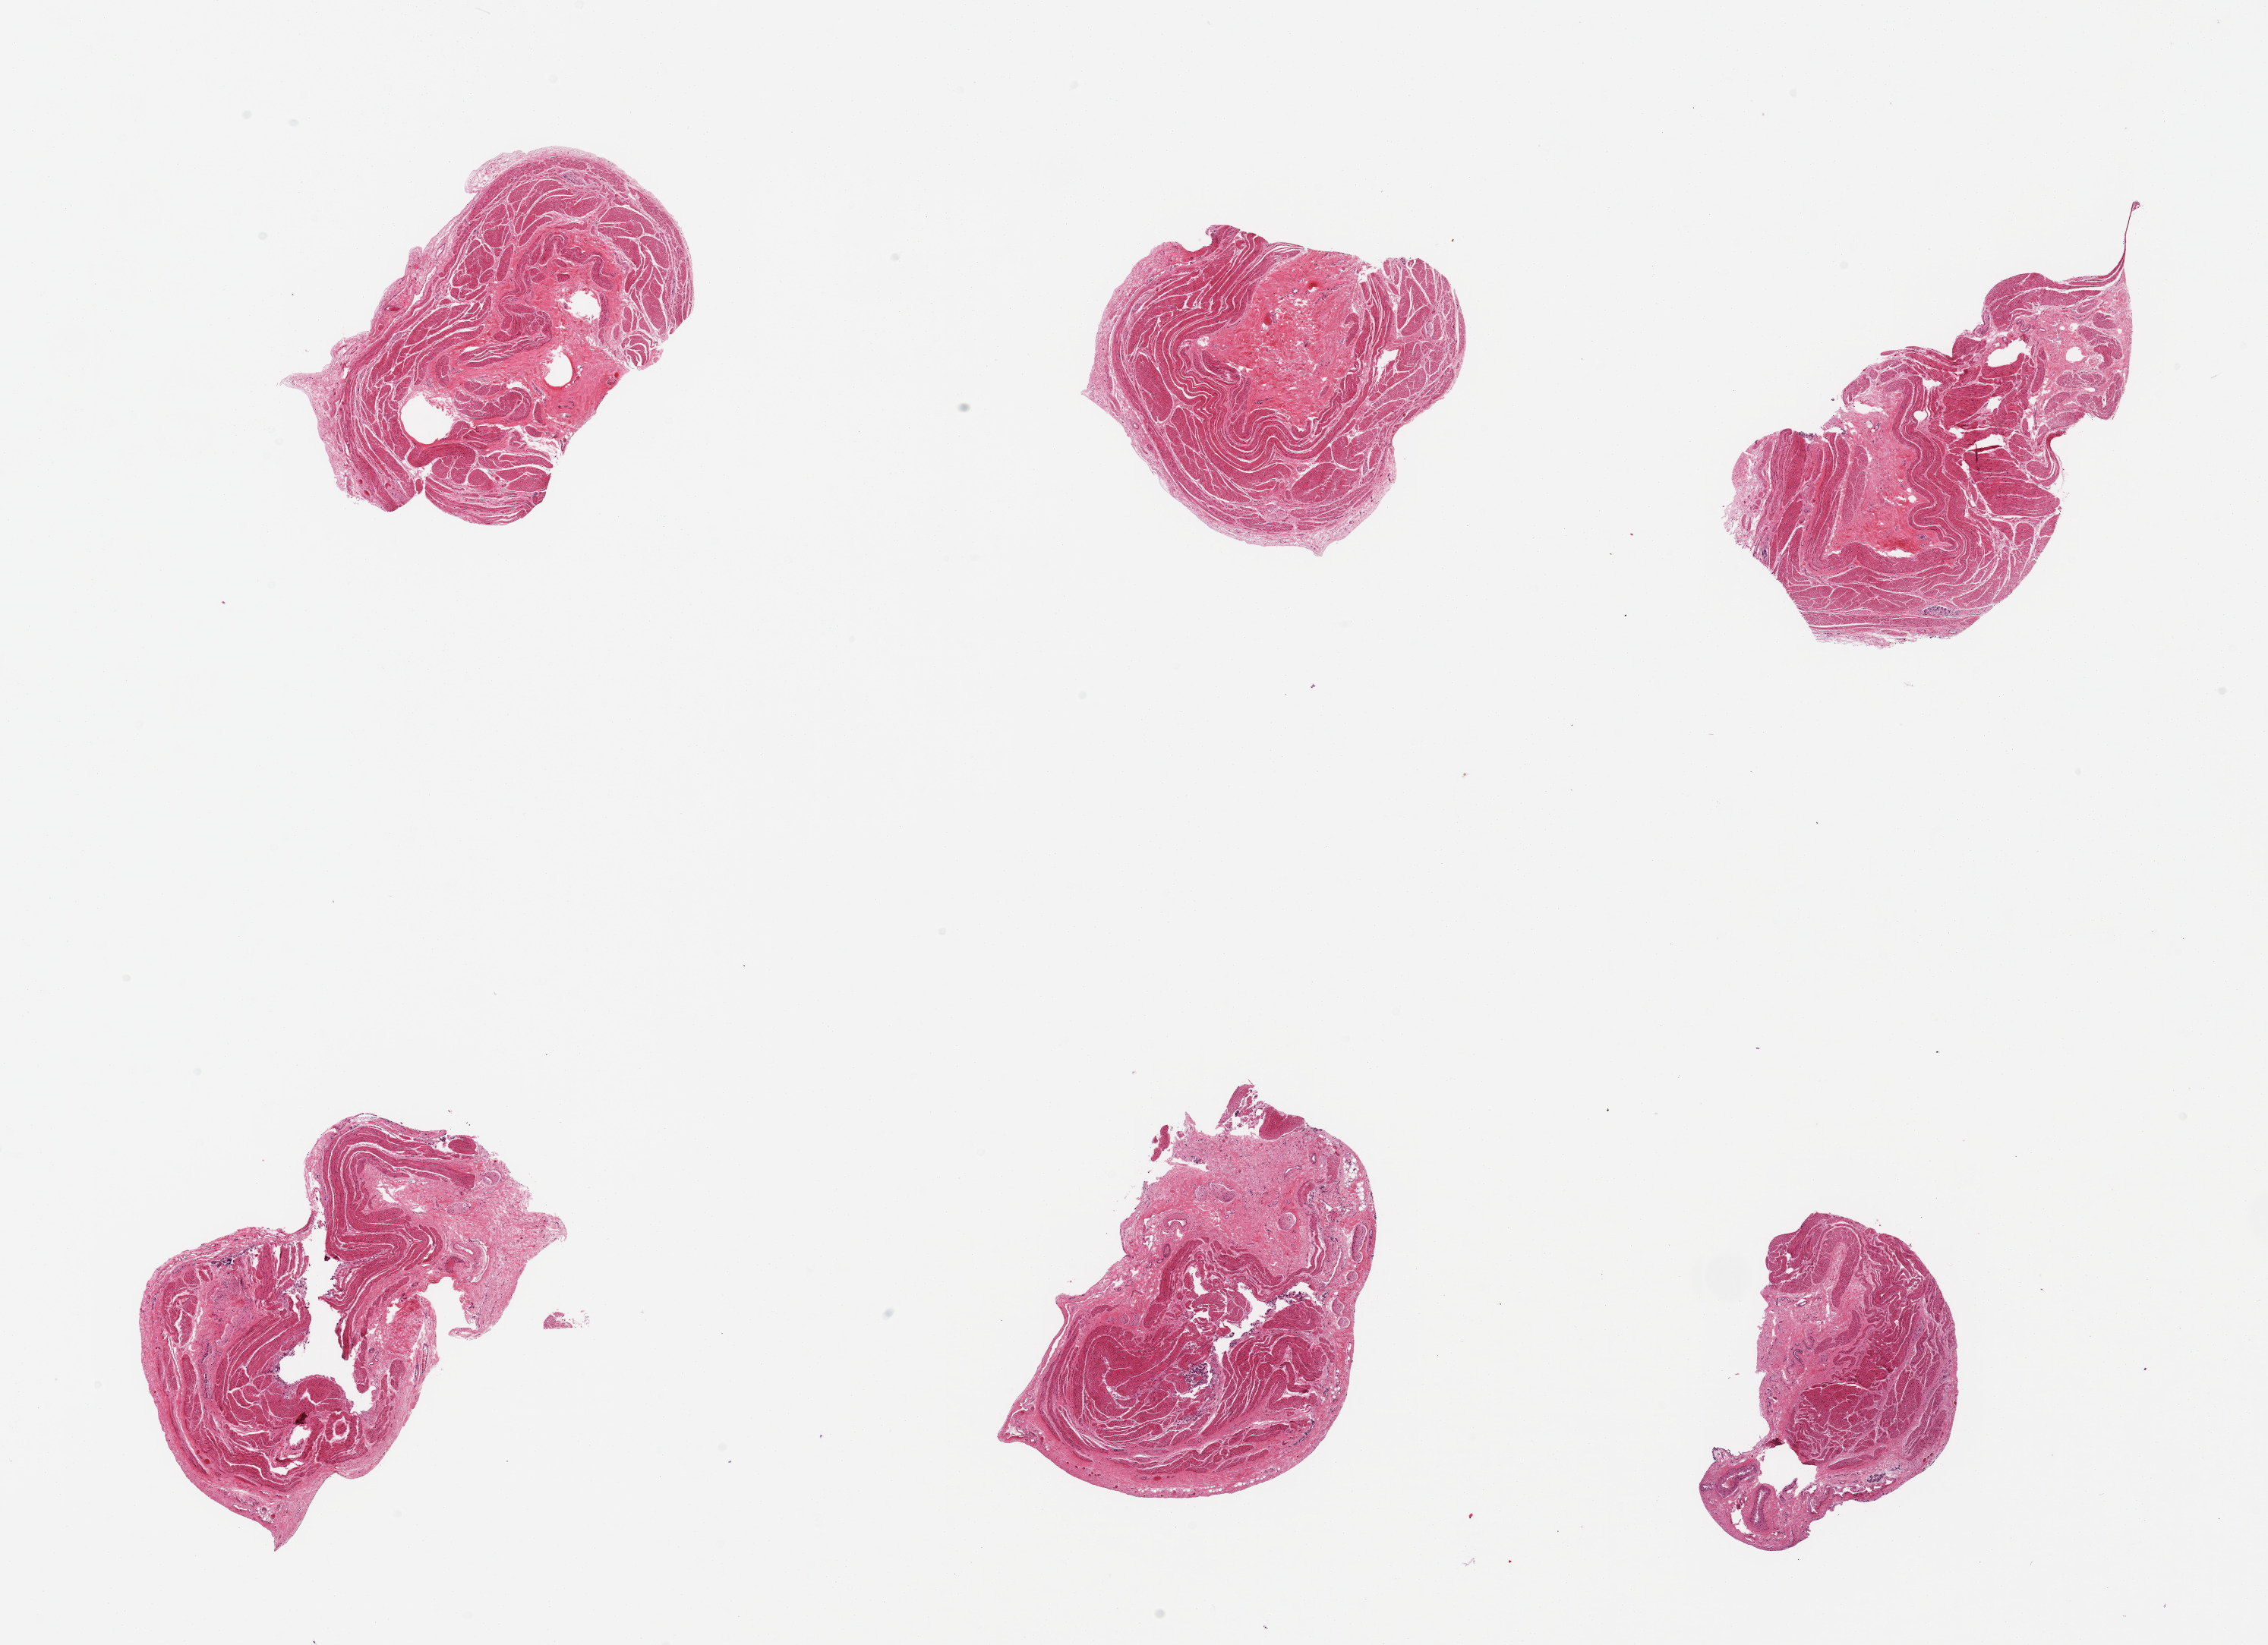
Whole-slide image, H&E stain, a low-resolution overview of the entire scanned area, about 23.6 x 17.1 mm (from a 20x scan), PAXgene-fixed paraffin-embedded (PFPE) section, target tissue: stomach, tissue donor sample. Male donor.
• reviewer comment on this tissue sample: 6 pieces, target mucosa completely sloughed; muscularis only